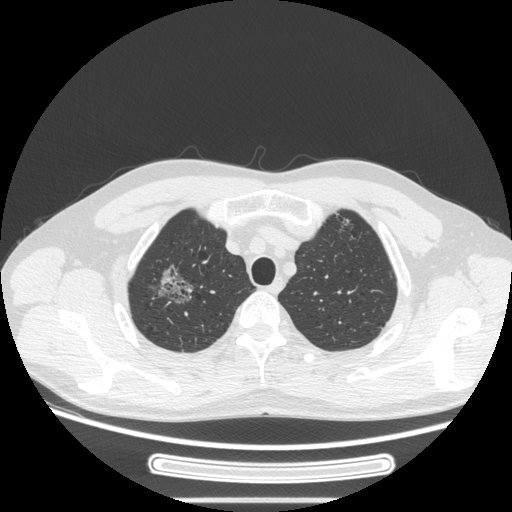
Chest CT, one axial slice. Position 222 of 269 along the scan axis. Reconstruction kernel STANDARD. Lung window (W 1500 / L -600 HU). 1.25 mm slice thickness. 512 × 512 image matrix, field of view 382 × 382 mm. Patient: male, 53 years. Case-level facts recorded for this patient, not image findings: clinical TNM (as recorded): T1c N0 M0.
Outlined on this slice (rectangle marked by the reading radiologist):
- lung tumour (recorded histology: adenocarcinoma): box from (x=149, y=261) to (x=201, y=315) px